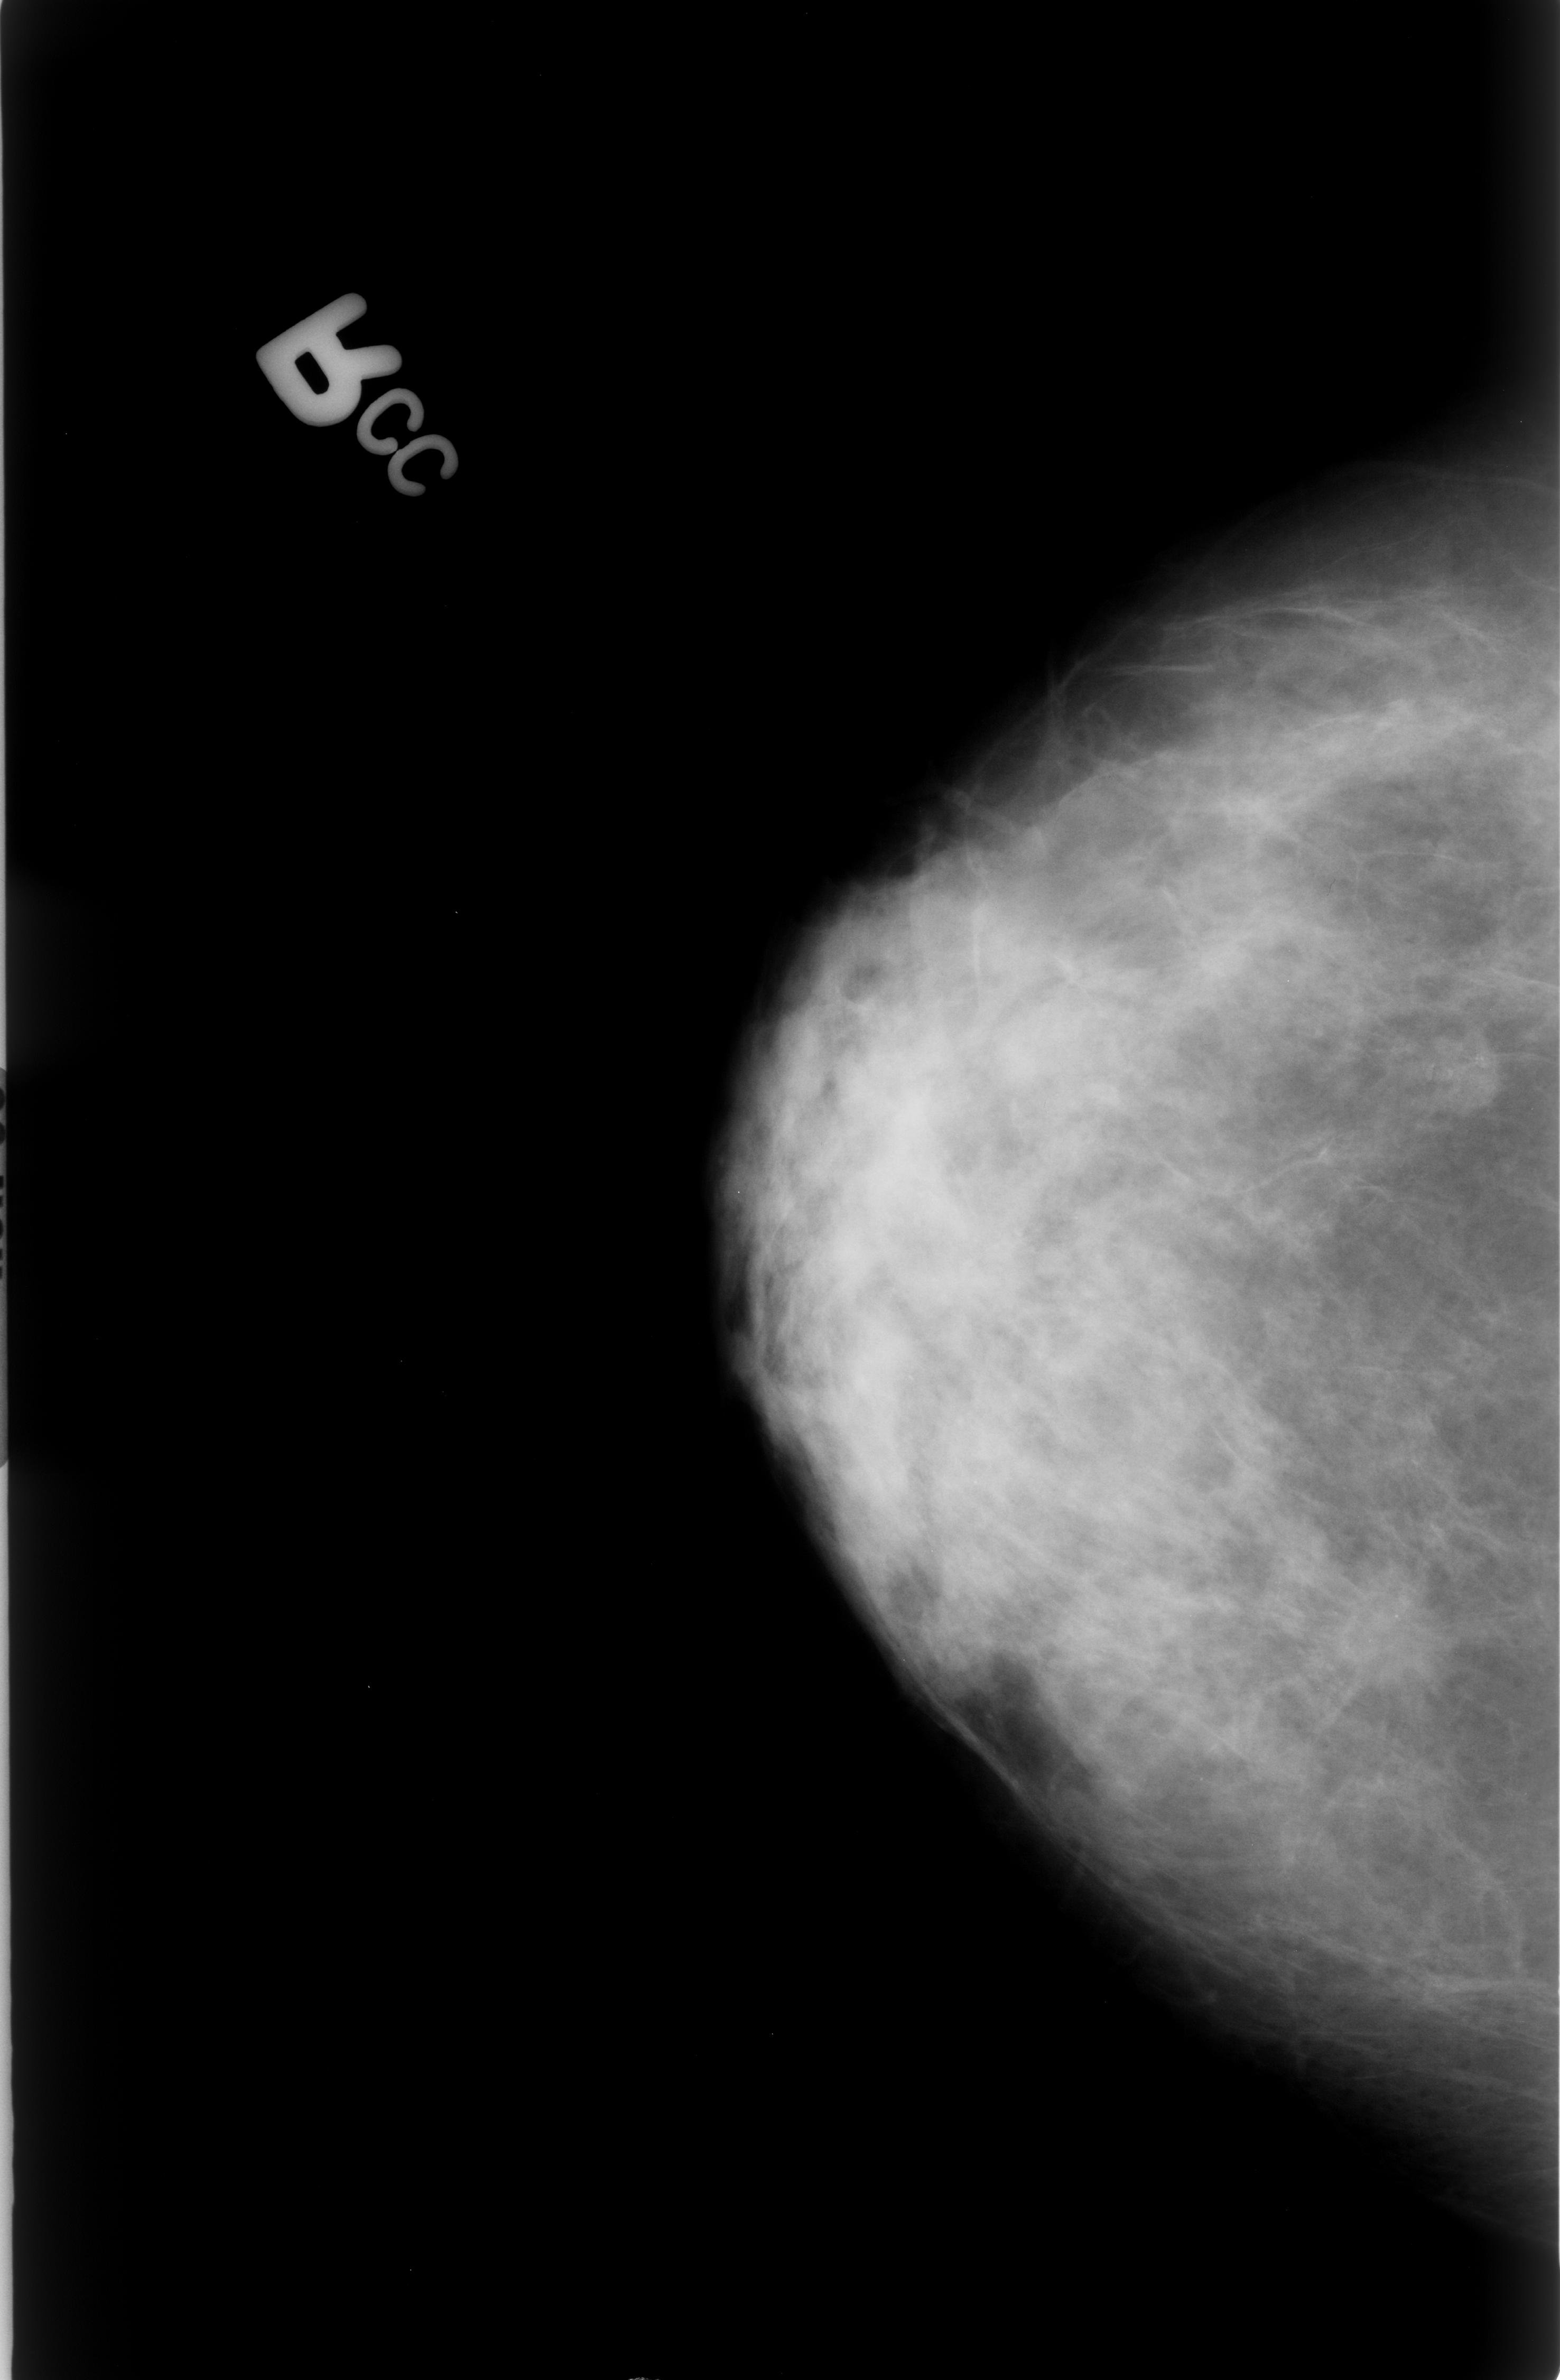
Digitized screen-film mammogram; right breast; CC view; breast composition: heterogeneously dense (BI-RADS density category 3 of 4).
- Marked findings (only marked abnormalities are described; nothing is implied about the rest of the image): calcifications, morphology punctate, distribution clustered; BI-RADS assessment category 4; pathology result (as recorded, not read from the image): malignant.